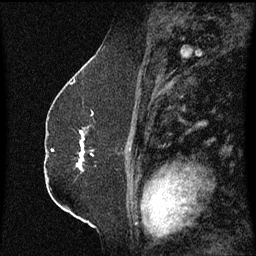
Breast MRI (dynamic contrast-enhanced), one sagittal slice. Slice 37 of 60 in the series (ordered by position). Dynamic contrast-enhanced series, image 2 of 3 at this slice position (ordered by acquisition). 1.5 T. TE 4.2 ms, TR 8.4 ms. 2.3 mm slice thickness. 256 × 256 image matrix, field of view 200 × 200 mm. Patient: female, 52 years. Case-level facts recorded for this patient, not image findings: setting: breast cancer imaged before/during neoadjuvant chemotherapy; receptor status: HR-positive, HER2-negative.
Structures marked on this image (semi-automatic segmentation, software-assisted and operator-edited):
- analysis volume of interest (the breast-tissue region the enhancement analysis was run in; not a lesion): bounding box <77,128,95,173> (left, top, right, bottom; pixels)
- tumour enhancement mask (voxels above the 70 % enhancement threshold inside the analysis volume of interest): <78,132,85,169>